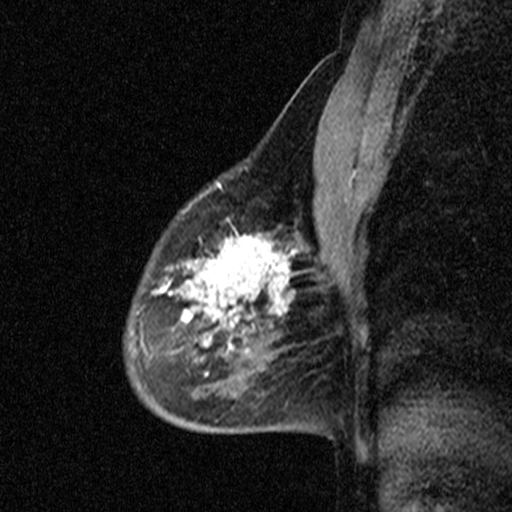
Breast MRI (dynamic contrast-enhanced), one sagittal slice; slice 30 of 44 in the series (ordered by position); dynamic contrast-enhanced study with each time point stored as its own series, time point 2 of 3 at this slice position (early post-contrast, ordered by acquisition time); 1.5 T; TE 4.5 ms, TR 11 ms; 3 mm slice thickness; 512 × 512 image matrix. Patient: female, 53 years. From the clinical record (not read from this slice): setting: breast cancer imaged before/during neoadjuvant chemotherapy; receptor status: HR-positive, HER2-negative.
Outlined on this slice (semi-automatically segmented with operator editing):
- analysis volume of interest (the breast-tissue region the enhancement analysis was run in; not a lesion): box from (x=88, y=176) to (x=313, y=423) px
- tumour enhancement mask (voxels above the 90 % enhancement threshold inside the analysis volume of interest): (x=160, y=214)–(x=296, y=374)